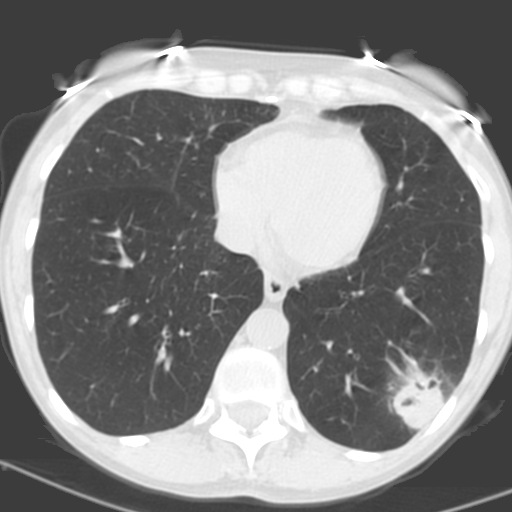
Low-dose screening chest CT, one axial slice; slice 54 of 156 in the series (ordered by position); 120 kVp; lung window (W 1500 / L -600 HU); 3.2 mm slice thickness; 512 × 512 image matrix, field of view 262 × 262 mm.
Outlined on this slice (manually delineated by an expert):
- lesion 1 (tumor, lower lobe of left lung): bounding box [x1, y1, x2, y2] px = [391, 368, 445, 428]